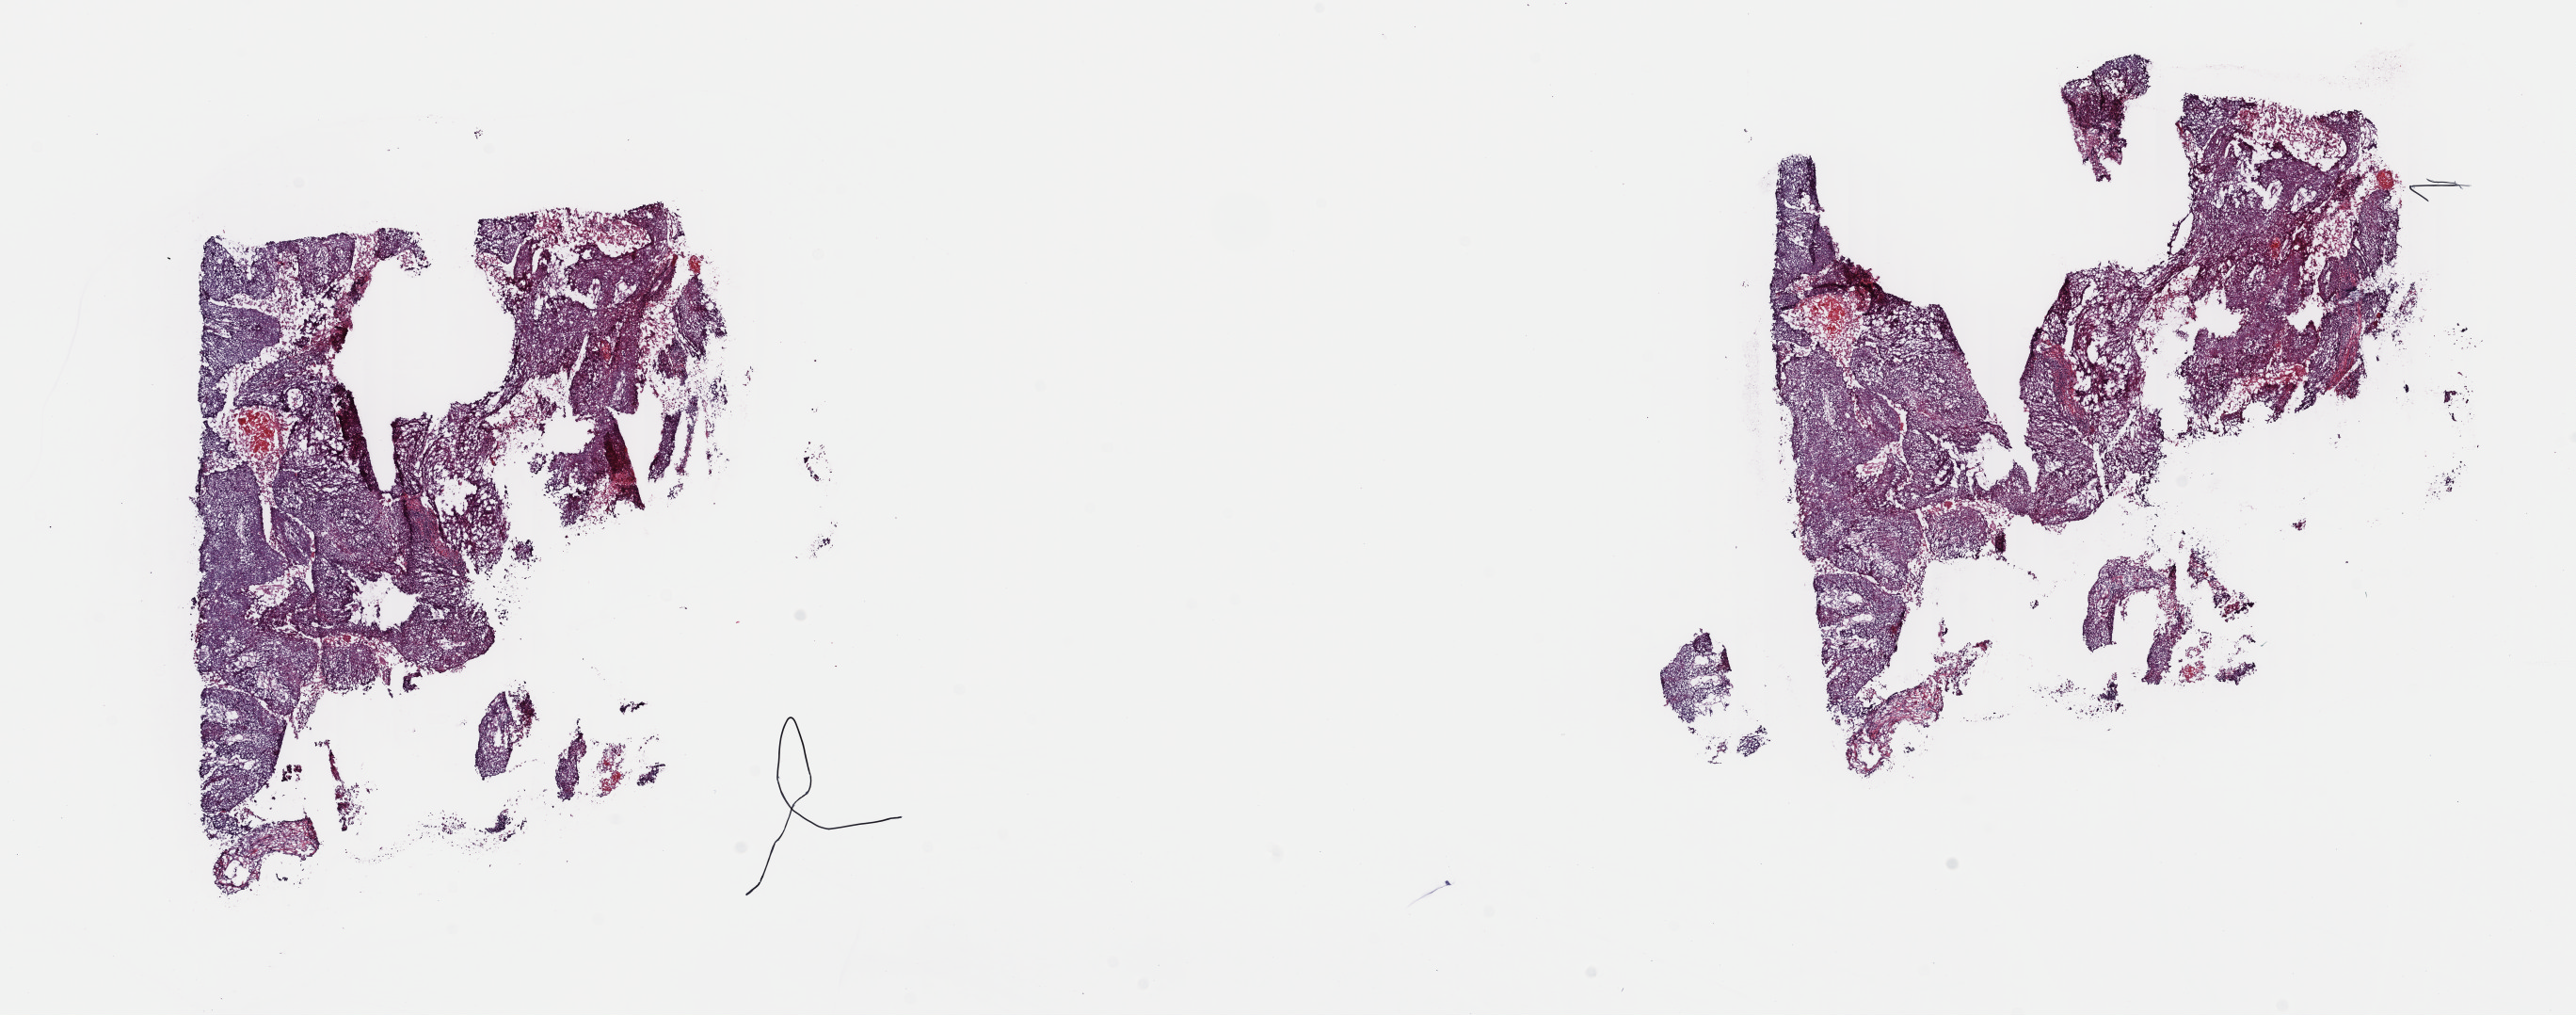
Digitized H&E-stained tissue section (whole slide), a low-resolution overview of the entire scanned area, about 21.6 x 8.5 mm (from a 40x scan); frozen section from the top of the tissue portion; cervix, primary tumour sample. Female, age 68 years at initial diagnosis. Histologic grade: G1 (well differentiated). Pathologist review of this section (percent, as recorded): tumour cells 98%, tumour nuclei 80%, normal cells 0%, stromal cells 0%, necrosis 2%. Infiltration values recorded for this section: lymphocyte infiltration 3%, monocyte infiltration 0%, neutrophil infiltration 0%.
• FIGO stage: IIA2
• histologic diagnosis: Squamous cell carcinoma, keratinizing, NOS